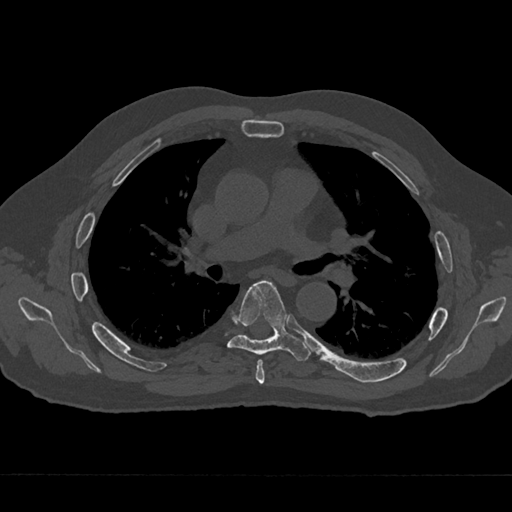
CT including the spine, one axial slice. Slice 428 of 797 in the series (ordered by position). Reconstruction kernel Br40s/3. 120 kVp. Bone window (W 1800 / L 400 HU). 0.5 mm slice thickness. 512 × 512 image matrix. Male patient, age 75 years. Case-level facts recorded for this patient, not image findings: primary cancer: renal.
Structures marked on this image (semi-automatically segmented with operator editing):
- T5 vertebra: bounding box <255,359,265,385> (left, top, right, bottom; pixels)
- T6 vertebra: <227,280,310,361>